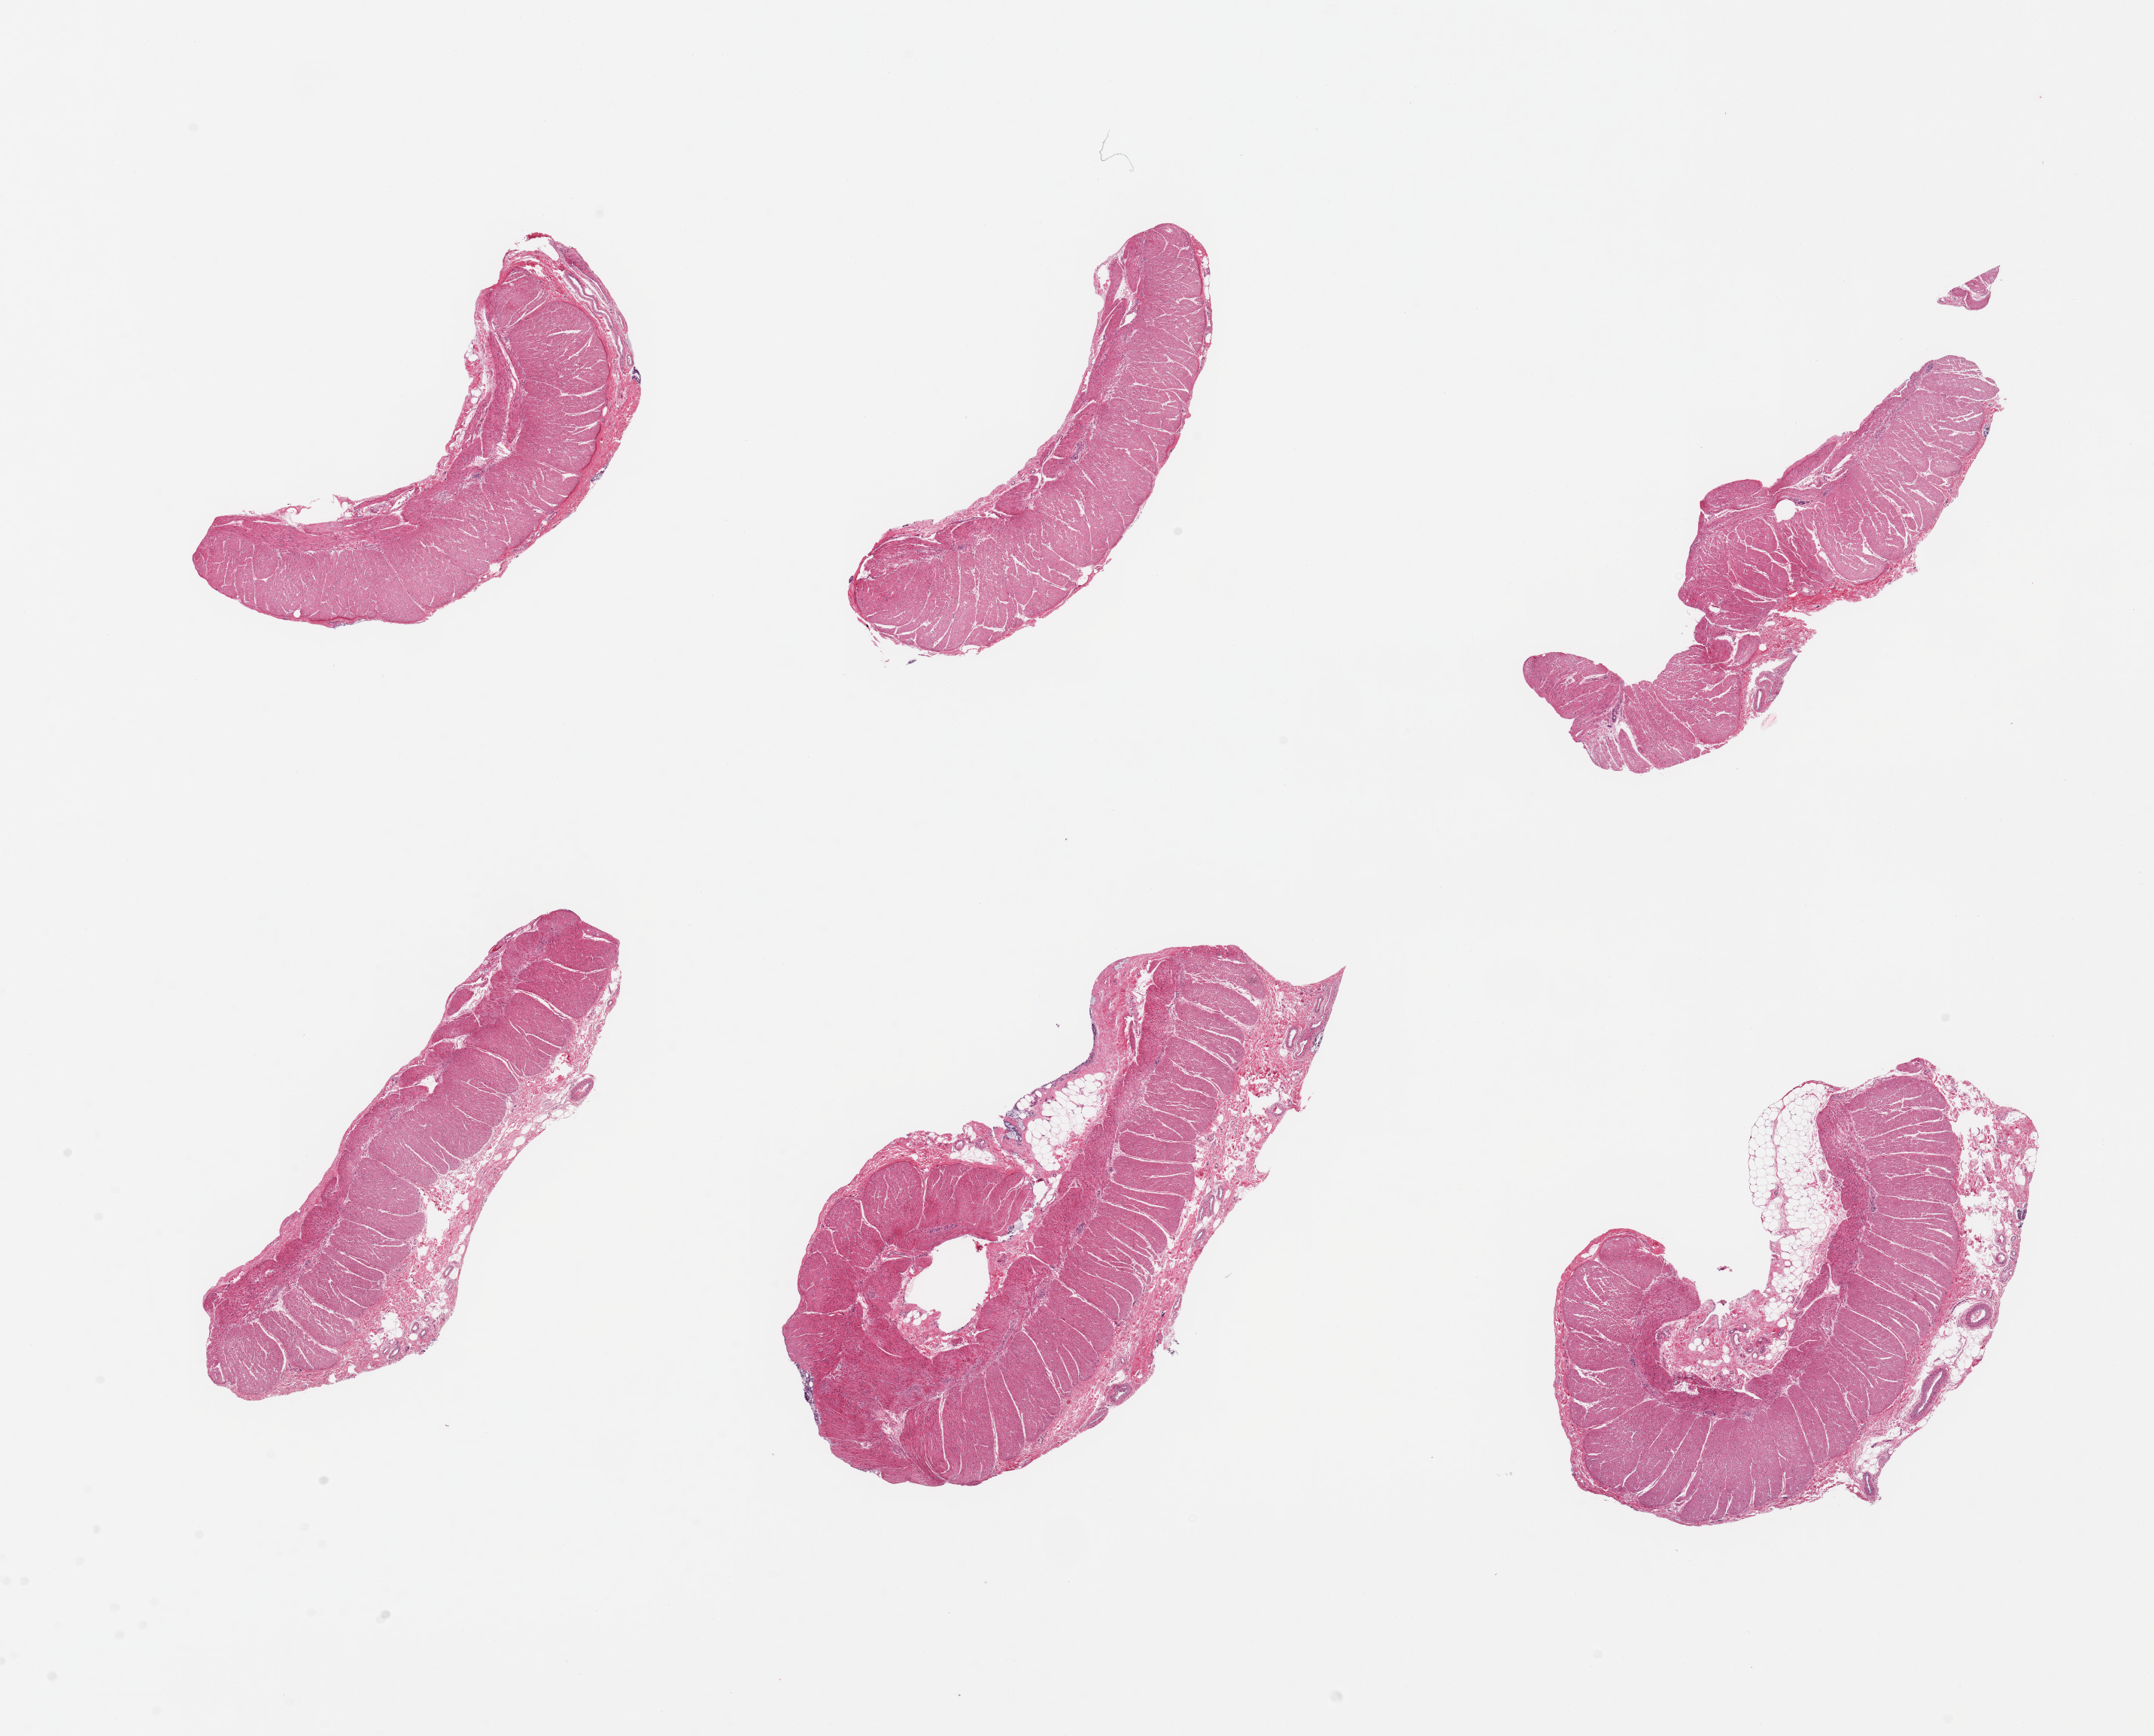
H&E whole-slide image, low-resolution overview of the scanned area, about 22.6 x 18.3 mm; PAXgene-fixed, paraffin-embedded tissue; target tissue: sigmoid colon; donor tissue sample. Male donor.
* reviewer comment on this tissue sample: 6 pieces; confirmed target muscularis. Adherent fat up to ~0.8mm